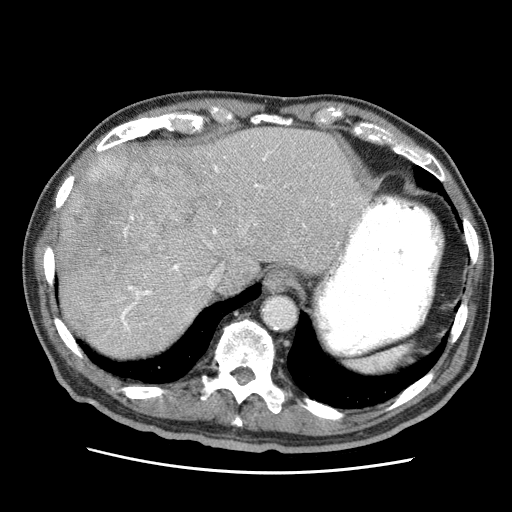
Contrast-enhanced abdominal CT (liver protocol), one axial slice. Position 51 of 75 along the scan axis. Reconstruction kernel STANDARD. Soft-tissue window (W 400 / L 40 HU). 512 × 512 image matrix, field of view 360 × 360 mm. From the clinical record (not read from this slice): diagnosis: hepatocellular carcinoma (patient treated with transarterial chemoembolisation; whether this scan precedes or follows treatment is not stated here); TNM stage (as recorded): Stage-IIIA; Child-Pugh class: A; tumour differentiation: well differentiated.
Structures marked on this image (semi-automatically segmented with operator editing):
- abdominal aorta: box from (x=264, y=296) to (x=297, y=329) px
- liver parenchyma outside the tumour (the mass and vessels are separate outlines, so this box may not span the whole liver): (x=55, y=127)–(x=368, y=356)
- mass: (x=61, y=146)–(x=219, y=335)
- liver vessels: (x=120, y=150)–(x=361, y=332)